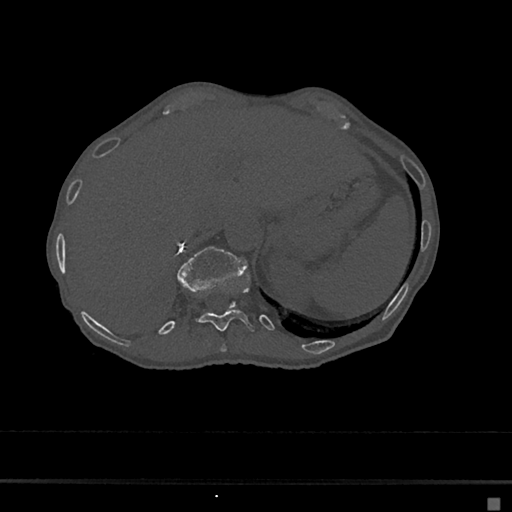
CT including the spine, one axial slice. Position 163 of 797 along the scan axis. Reconstruction kernel Br40s/3. Bone window (W 1800 / L 400 HU). 0.5 mm slice thickness. 512 × 512 image matrix. Patient: female, 68 years. From the clinical record (not read from this slice): primary cancer: renal.
Structures marked on this image (semi-automatically segmented with operator editing):
- T10 vertebra: bounding box (x1, y1, x2, y2) in pixels: (220, 344, 227, 353)
- T11 vertebra: (196, 285, 256, 332)
- T12 vertebra: (176, 247, 248, 307)